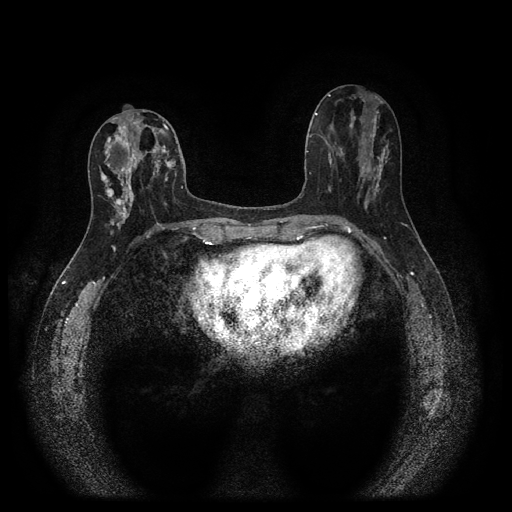
Breast MRI (dynamic contrast-enhanced, multi-phase), one axial slice. Position 46 of 116 along the scan axis. Dynamic contrast-enhanced series, time point 2 of 5 at this slice position (early post-contrast). 1.5 T. TE 2.7 ms, TR 5.4 ms. 2 mm slice thickness. 512 × 512 image matrix. Patient: female, 47 years.
Structures marked on this image (semi-automatically segmented with operator editing):
- breast lesion (labelled 'tumour' in the annotation; benign lesions carry a separate 'benign' label): box from (x=102, y=119) to (x=175, y=221) px
- breast lesion (labelled benign in the annotation): (x=105, y=187)–(x=114, y=198)